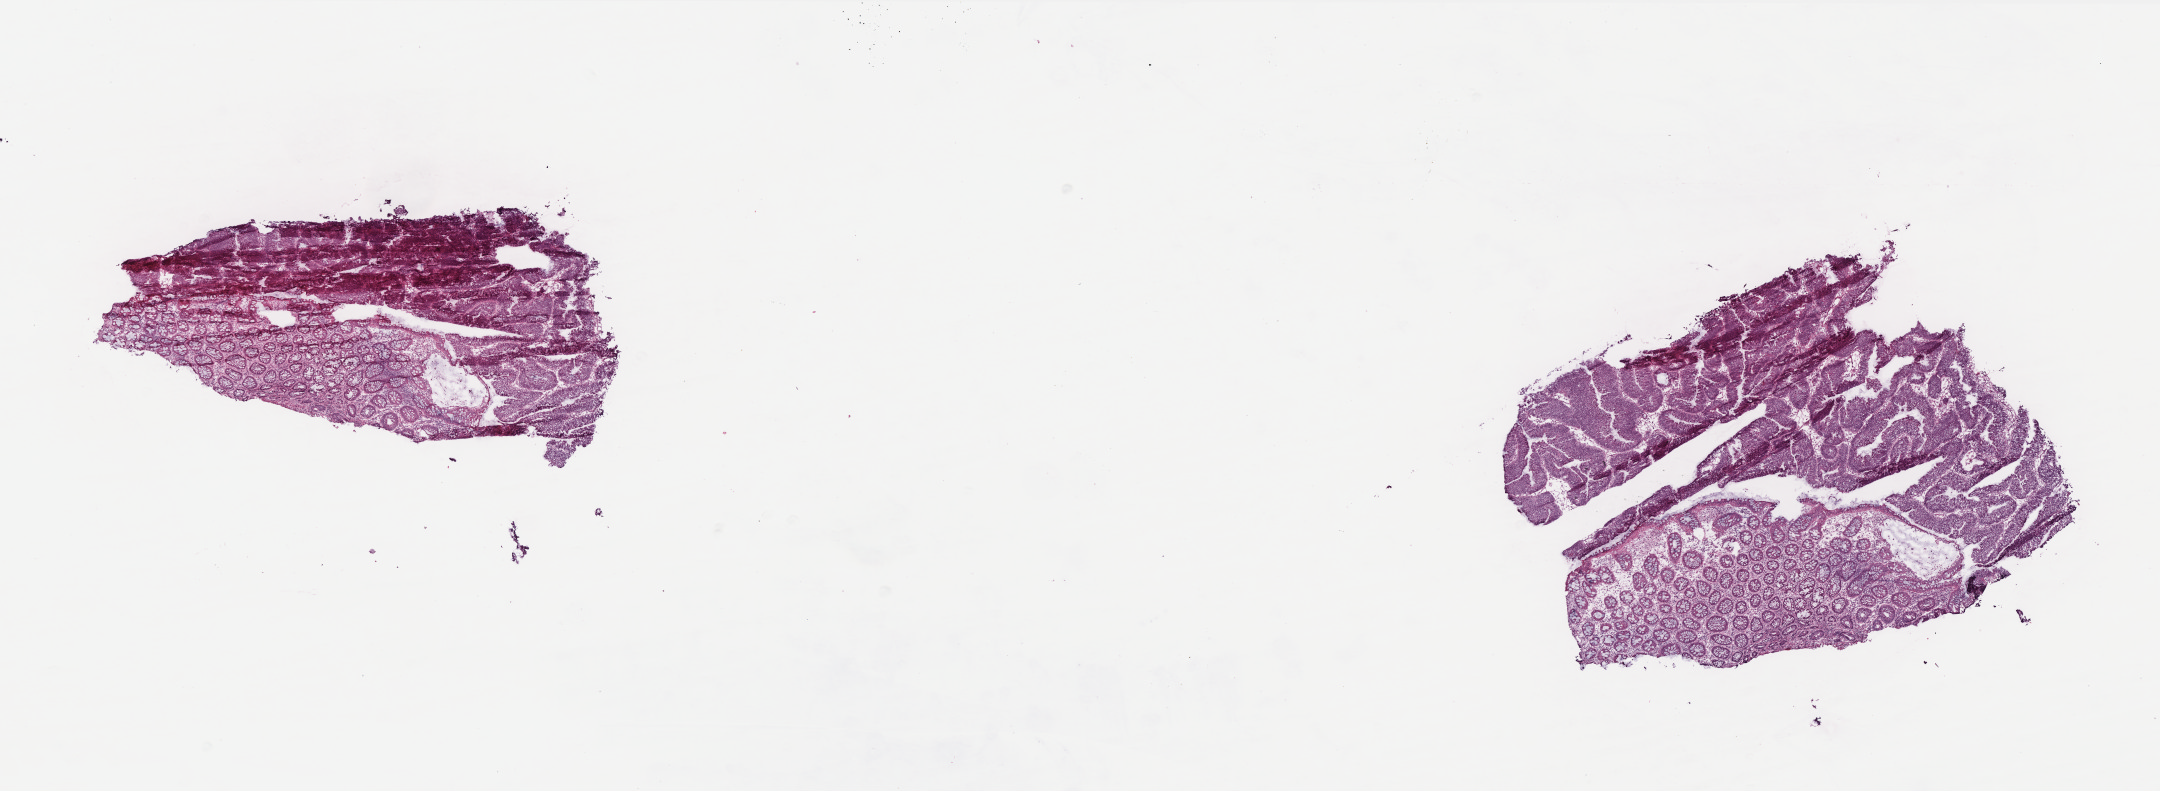
Whole-slide histology image, H&E-stained, shown as a low-resolution overview of the whole scanned area (about 17.3 x 6.3 mm, from a 40x scan). Frozen section from the top of the tissue portion. Rectum, primary tumour sample. Female patient; age at initial diagnosis 50 years. Slide review estimates, as recorded: tumour cells 60%, tumour nuclei 70%, normal cells 35%, stromal cells 4%, necrosis 1%. Infiltration values recorded for this section: lymphocyte infiltration 15%, monocyte infiltration 4%, neutrophil infiltration 1%.
AJCC pathologic stage: I (6th edition). Pathologic diagnosis: Mucinous adenocarcinoma. Lymph nodes positive (case pathology): 0 of 28 examined.